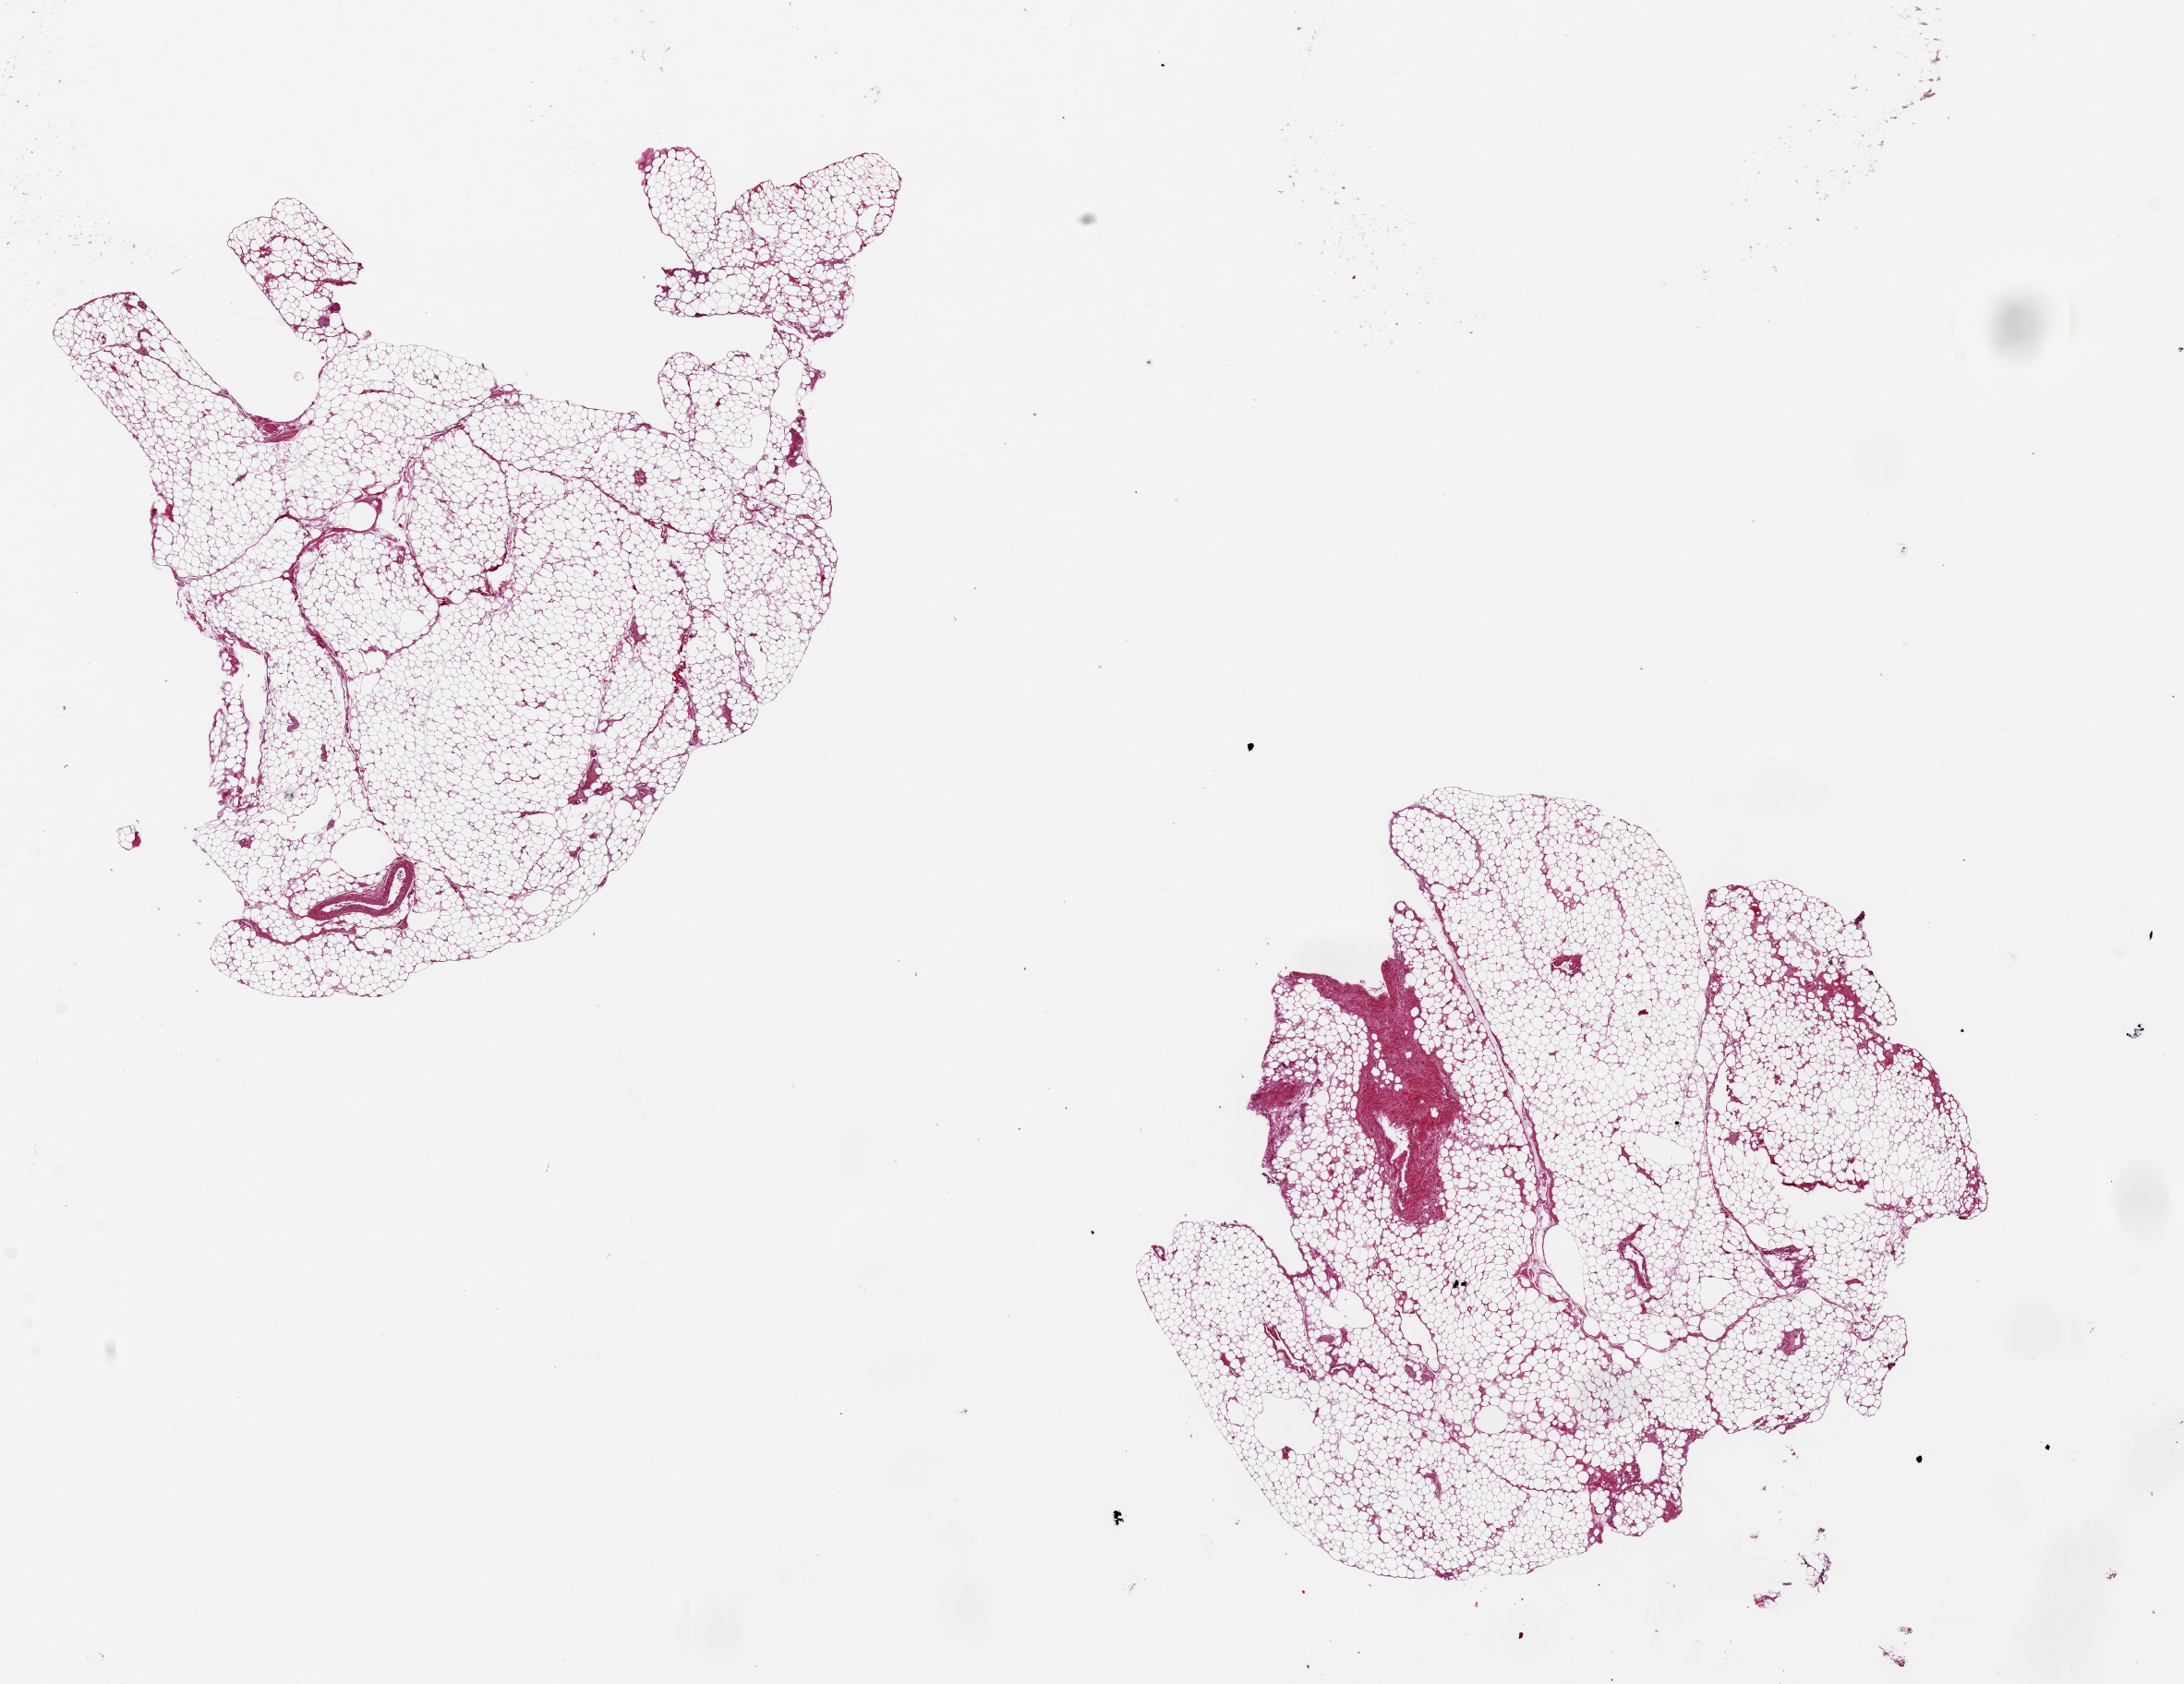
H&E whole-slide image — low-resolution overview of the scanned area, about 18.7 x 14.4 mm (slide scanned at 20x); PAXgene-fixed paraffin-embedded (PFPE) section; target tissue: omentum; tissue donor sample. Donor: male.
Reviewer comment on this tissue sample: 2 pieces, 9x6 & 7x6.5mm; no defects.